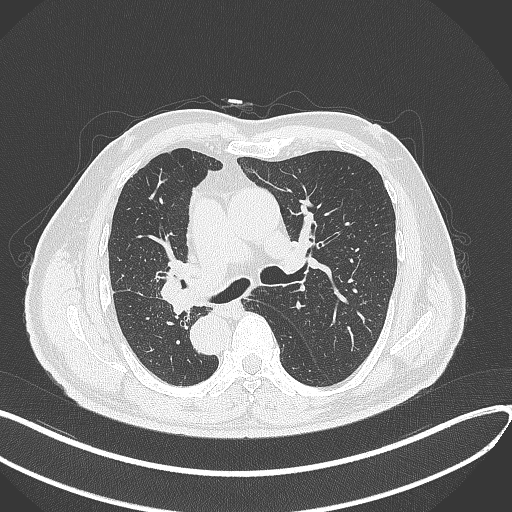
Chest CT, one axial slice; slice 178 of 300 in the series (ordered by position); reconstruction kernel B70f; lung window (W 1500 / L -600 HU); 512 × 512 image matrix, field of view 400 × 400 mm. Patient: male, 67 years. Case-level facts recorded for this patient, not image findings: clinical TNM (as recorded): T2a N0 M0.
Outlined on this slice (bounding box drawn by a radiologist):
- lung tumour (recorded histology: squamous cell carcinoma): bounding box (x1, y1, x2, y2) in pixels: (156, 256, 198, 313)